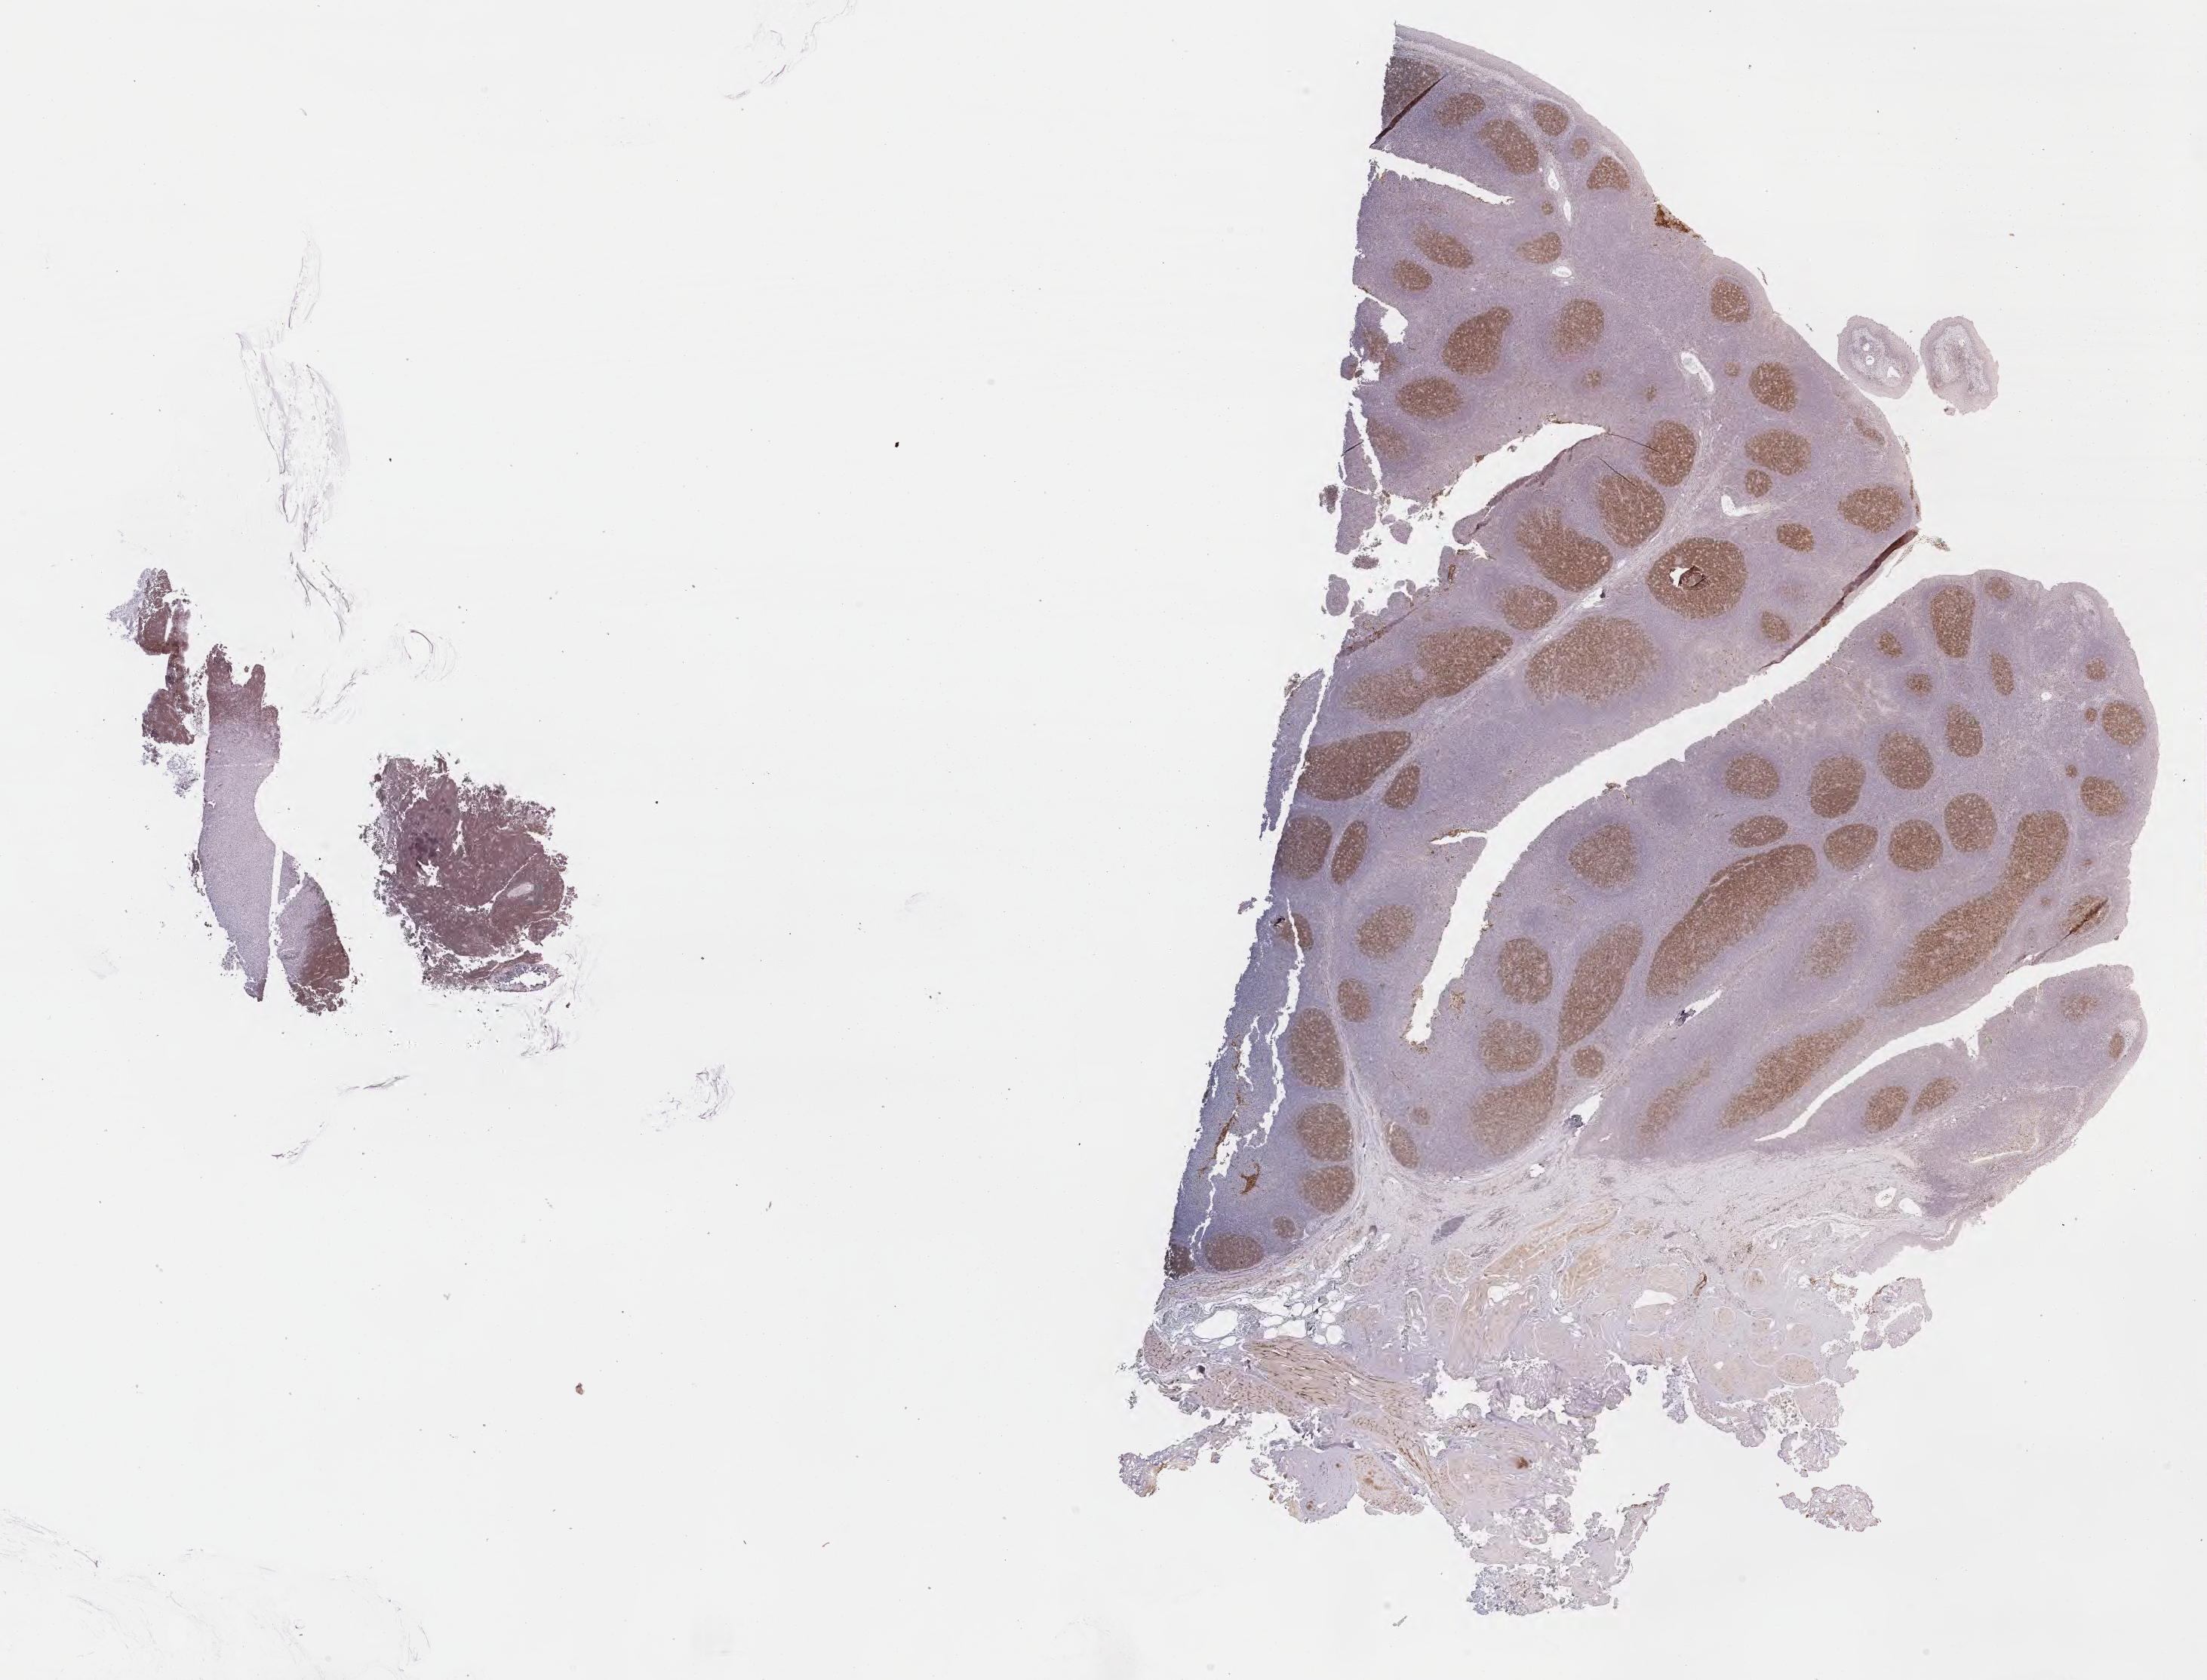
Whole-slide image, immunohistochemical stain for CD10, low-resolution overview of the scanned area, about 23.7 x 18.0 mm; specimen: tumor tissue; site: cranium. Male, age 4 years at initial diagnosis.
* diagnosis: Burkitt lymphoma, NOS